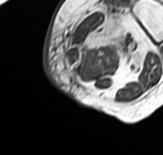
MRI of an extremity soft-tissue mass, one axial slice; MR volume resampled by the dataset authors to the PET/CT grid (not the native acquisition matrix); 3.27 mm slice thickness; 163 × 155 image matrix. Female patient. Case-level facts recorded for this patient, not image findings: histological type: pleomorphic leiomyosarcoma; grade: high; site of the primary tumour: left thigh.
Annotated regions visible in this slice (expert contour drawn on MRI and transferred to this co-registered scan by the dataset authors):
- gross tumour volume including surrounding oedema: box from (x=65, y=8) to (x=145, y=73) px